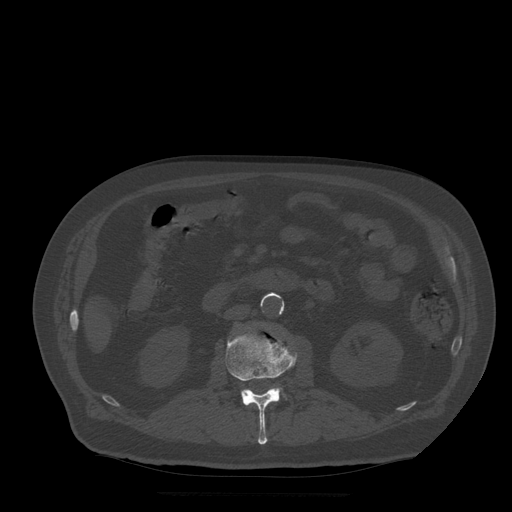
CT including the spine, one axial slice; slice 163 of 522 in the series (ordered by position); bone window (W 1800 / L 400 HU); 1.25 mm slice thickness; 512 × 512 image matrix, field of view 420 × 420 mm. Patient age 72 years. Case-level facts recorded for this patient, not image findings: primary cancer: prostate.
Outlined on this slice (semi-automatically segmented with operator editing):
- L2 vertebra: bounding box <226,332,298,445> (left, top, right, bottom; pixels)